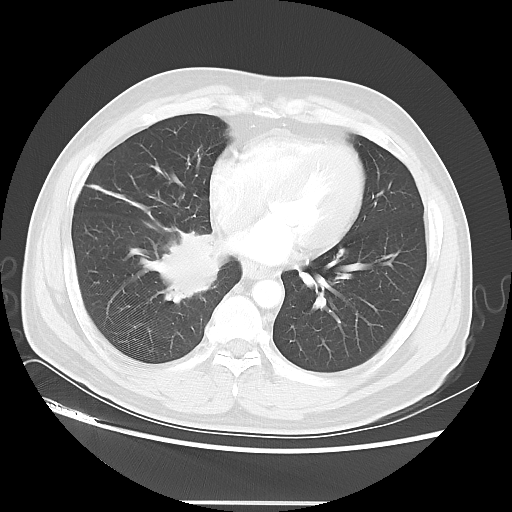
Chest CT, one axial slice. Slice 17 of 48 in the series (ordered by position). 120 kVp. Lung window (W 1500 / L -600 HU). 512 × 512 image matrix. Patient: male, 53 years. From the clinical record (not read from this slice): clinical TNM (as recorded): T2 N3 M0; histopathological grade: G3.
Outlined on this slice (rectangle marked by the reading radiologist):
- lung tumour (recorded histology: small cell carcinoma): bounding box [x1, y1, x2, y2] px = [146, 226, 222, 307]